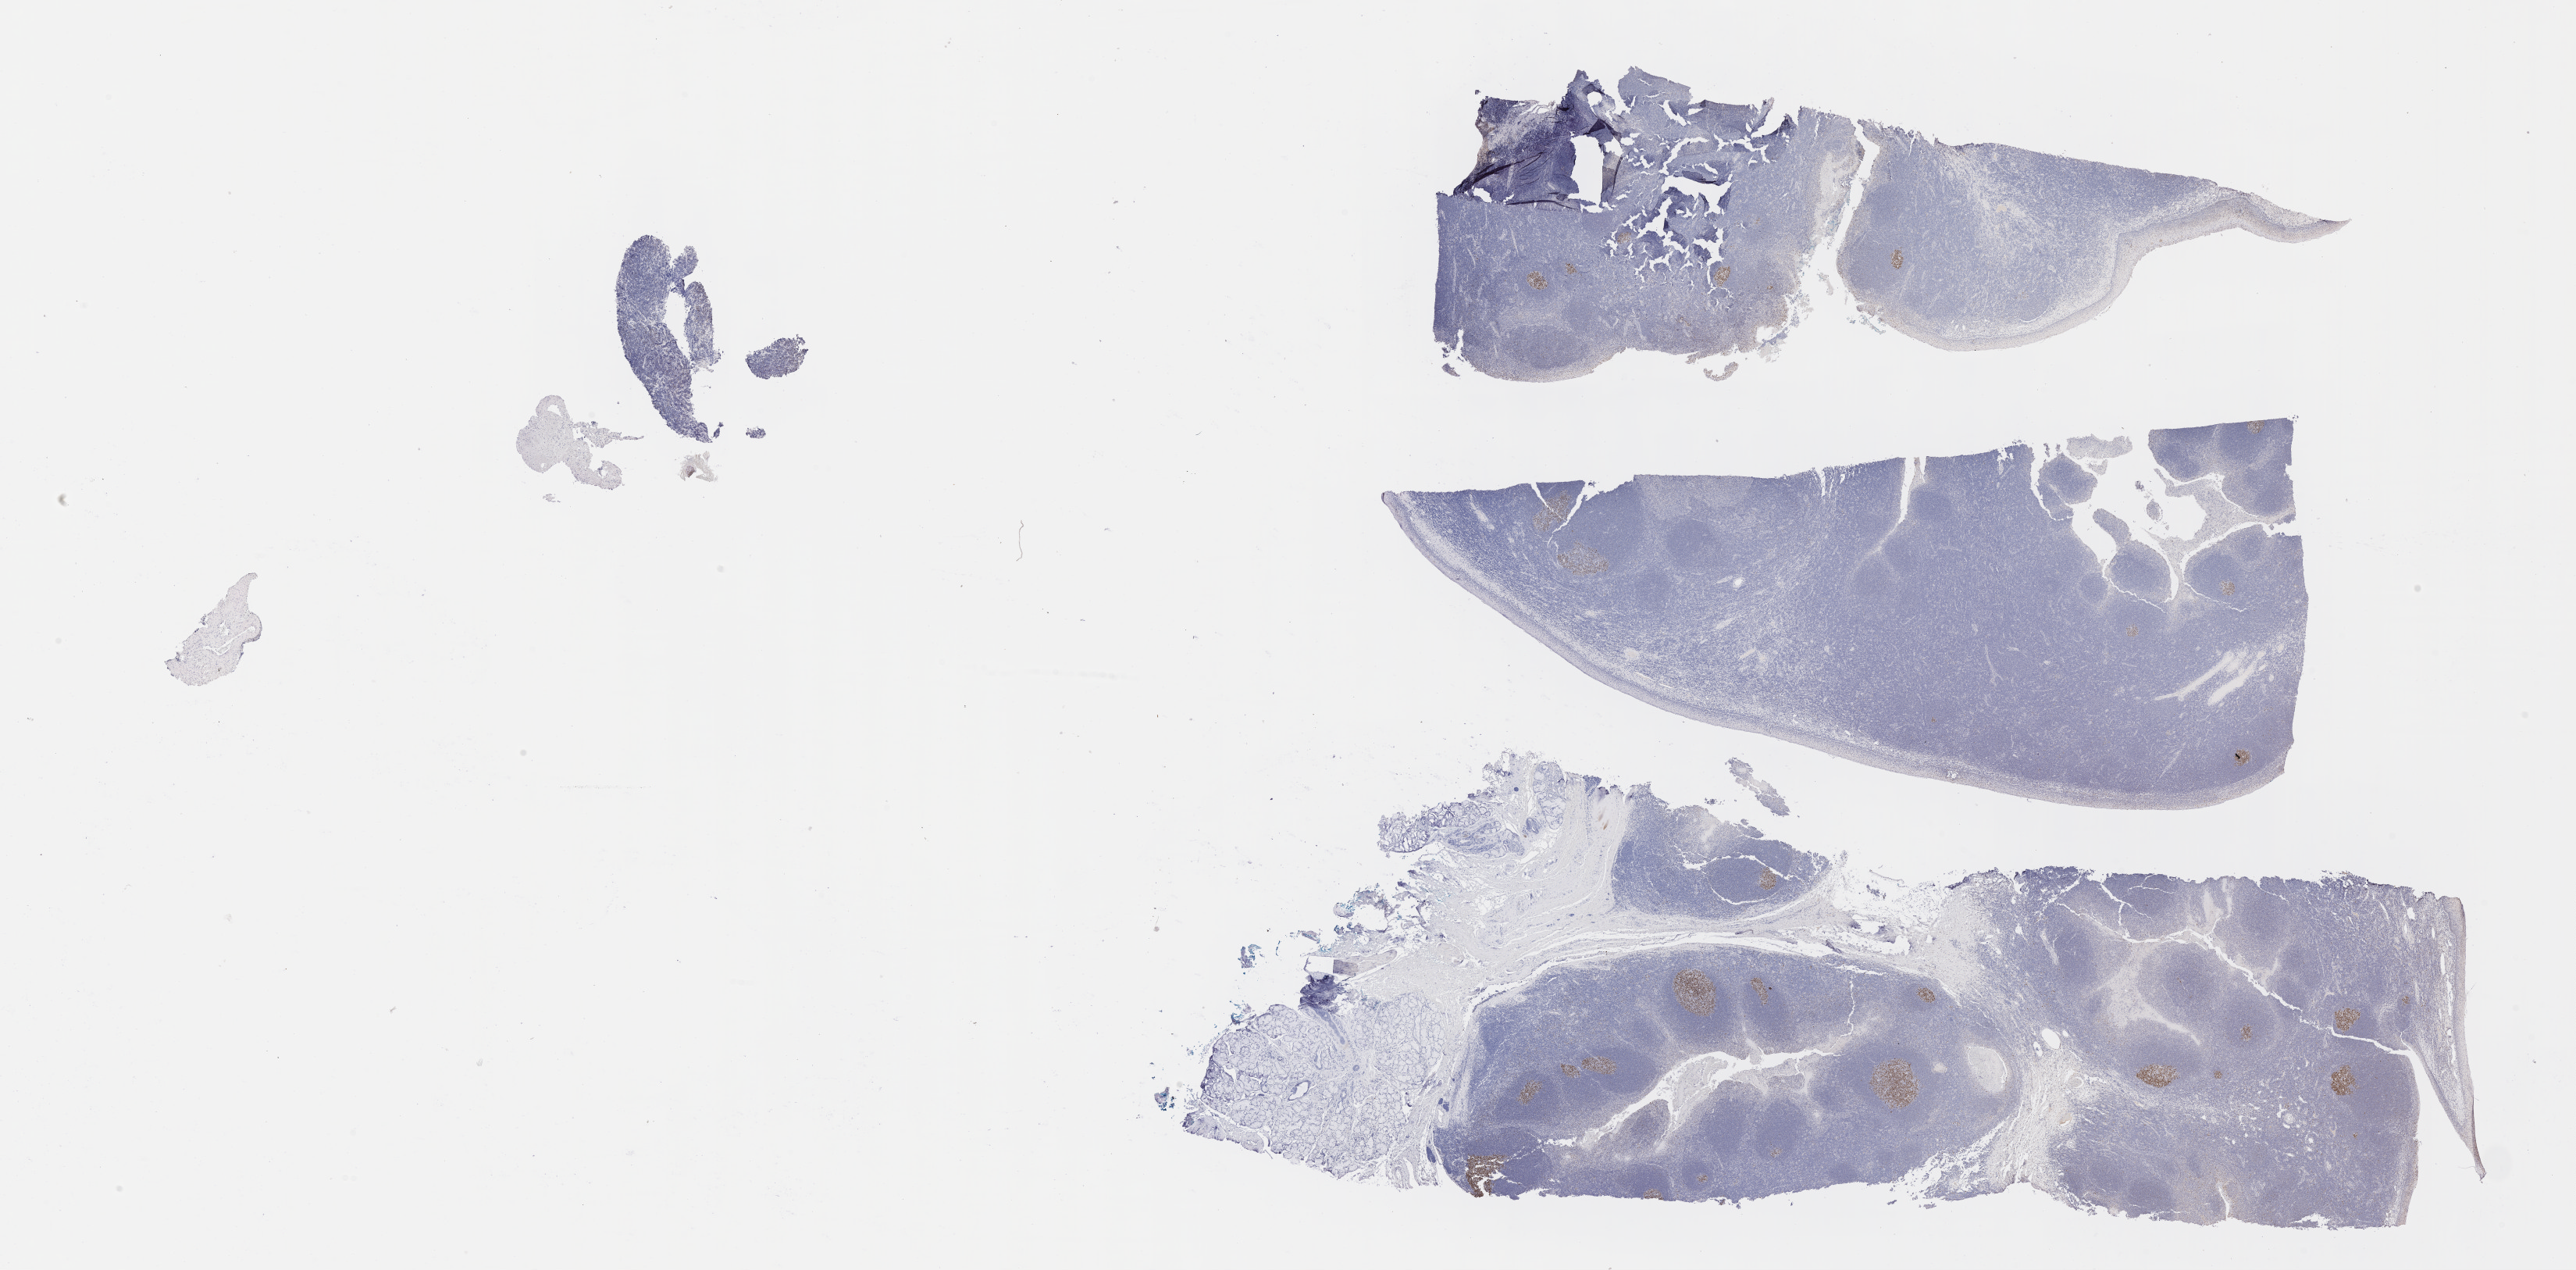
IHC for BCL6, whole-slide image, low-resolution overview of the scanned area, about 26.7 x 13.1 mm; tumor tissue; anatomic site: abdomen proper. Female, age 7 years at initial diagnosis.
* diagnosis: Burkitt lymphoma, NOS